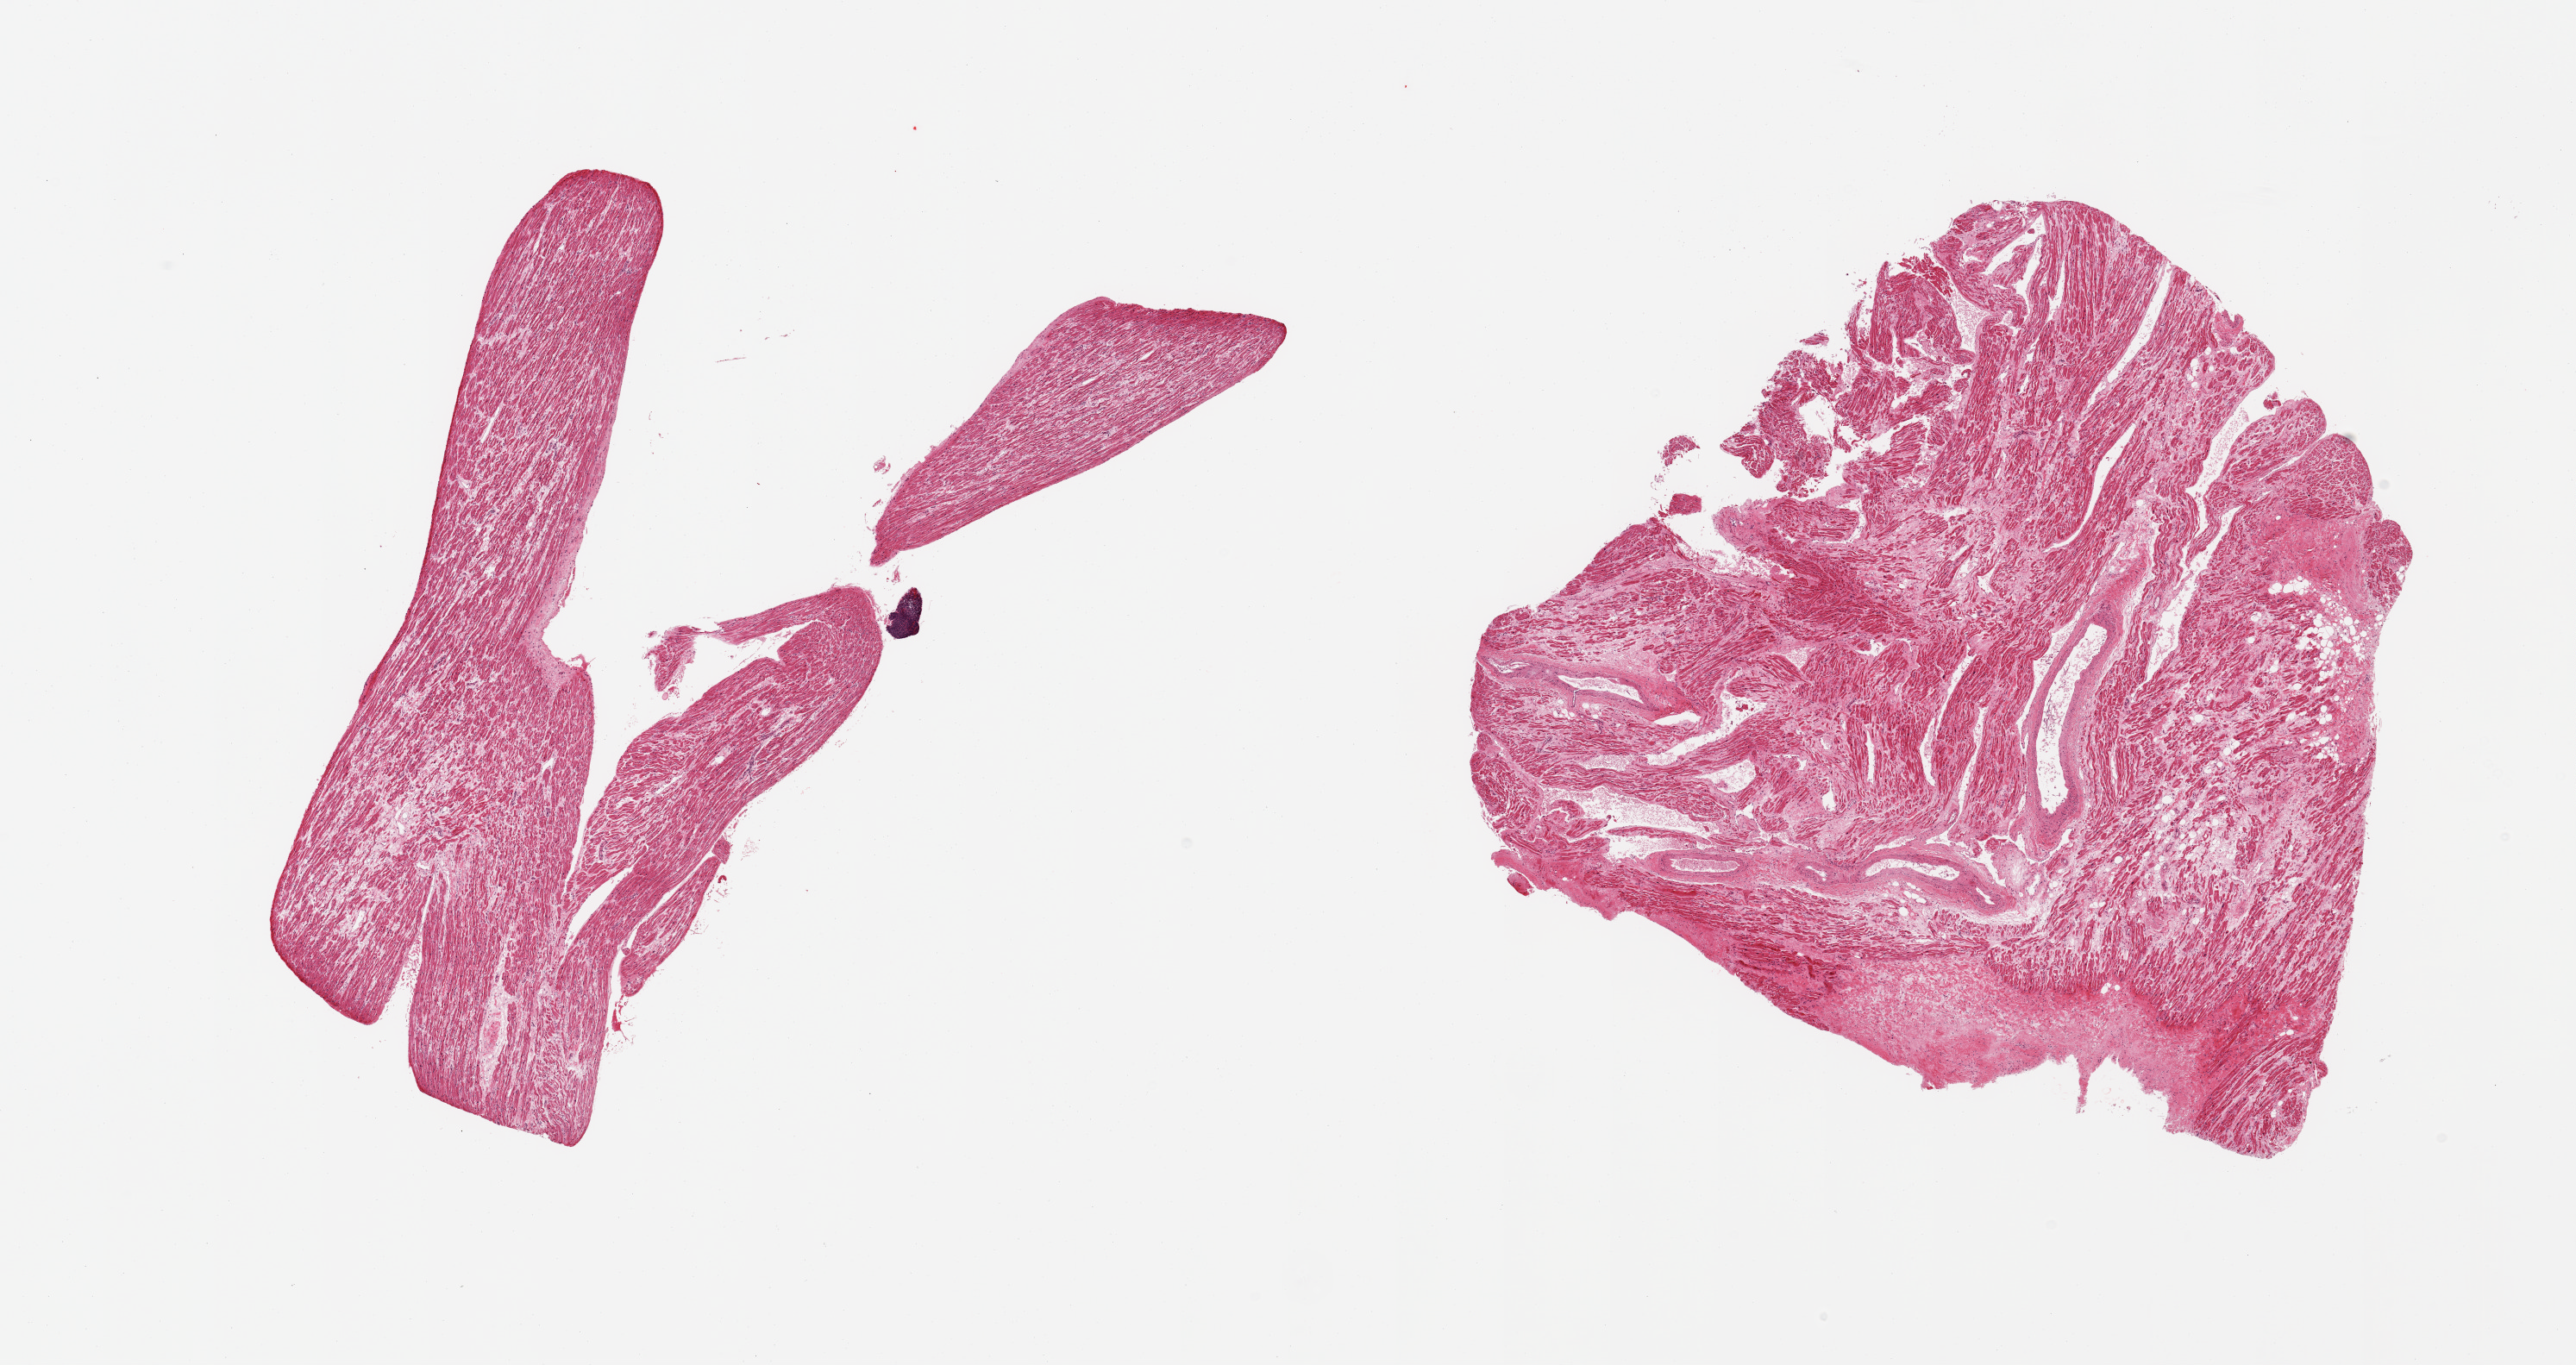
Hematoxylin and eosin (H&E) whole-slide image — whole scanned area (about 23.6 x 12.5 mm, from a 20x scan) shown as a low-resolution overview; PAXgene-fixed, paraffin-embedded tissue; target tissue: auricular appendage; tissue donor sample. Donor: female.
Pathologist's review note for this sample: 2 pieces.